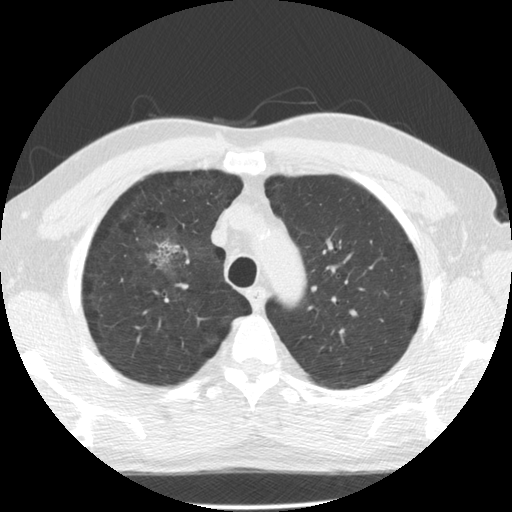
Chest CT (low-dose screening protocol), one axial image, second annual screen, lung window (W 1500 / L -600 HU), 2.5 mm slice thickness, slice 101 of 135 in the series. Male participant, aged 60 years at enrolment. Former smoker at enrolment.
Lesion marked by an expert reader, bounding box [x1, y1, x2, y2] px = [134, 224, 194, 284]. Reader record for this screening exam (exam-level; its link to the box is not recorded): non-calcified nodule or mass ≥4 mm, right upper lobe, poorly defined margins, mixed attenuation, pre-existing on the prior screen: yes; interval growth: yes. Official screen result: positive, other. Participant outcome: lung cancer diagnosed 562 days after this screen (after the third annual screen) — papillary adenocarcinoma, NOS, right upper lobe, moderately differentiated (G2), stage IB (AJCC 6th edition), 32 mm at pathology.